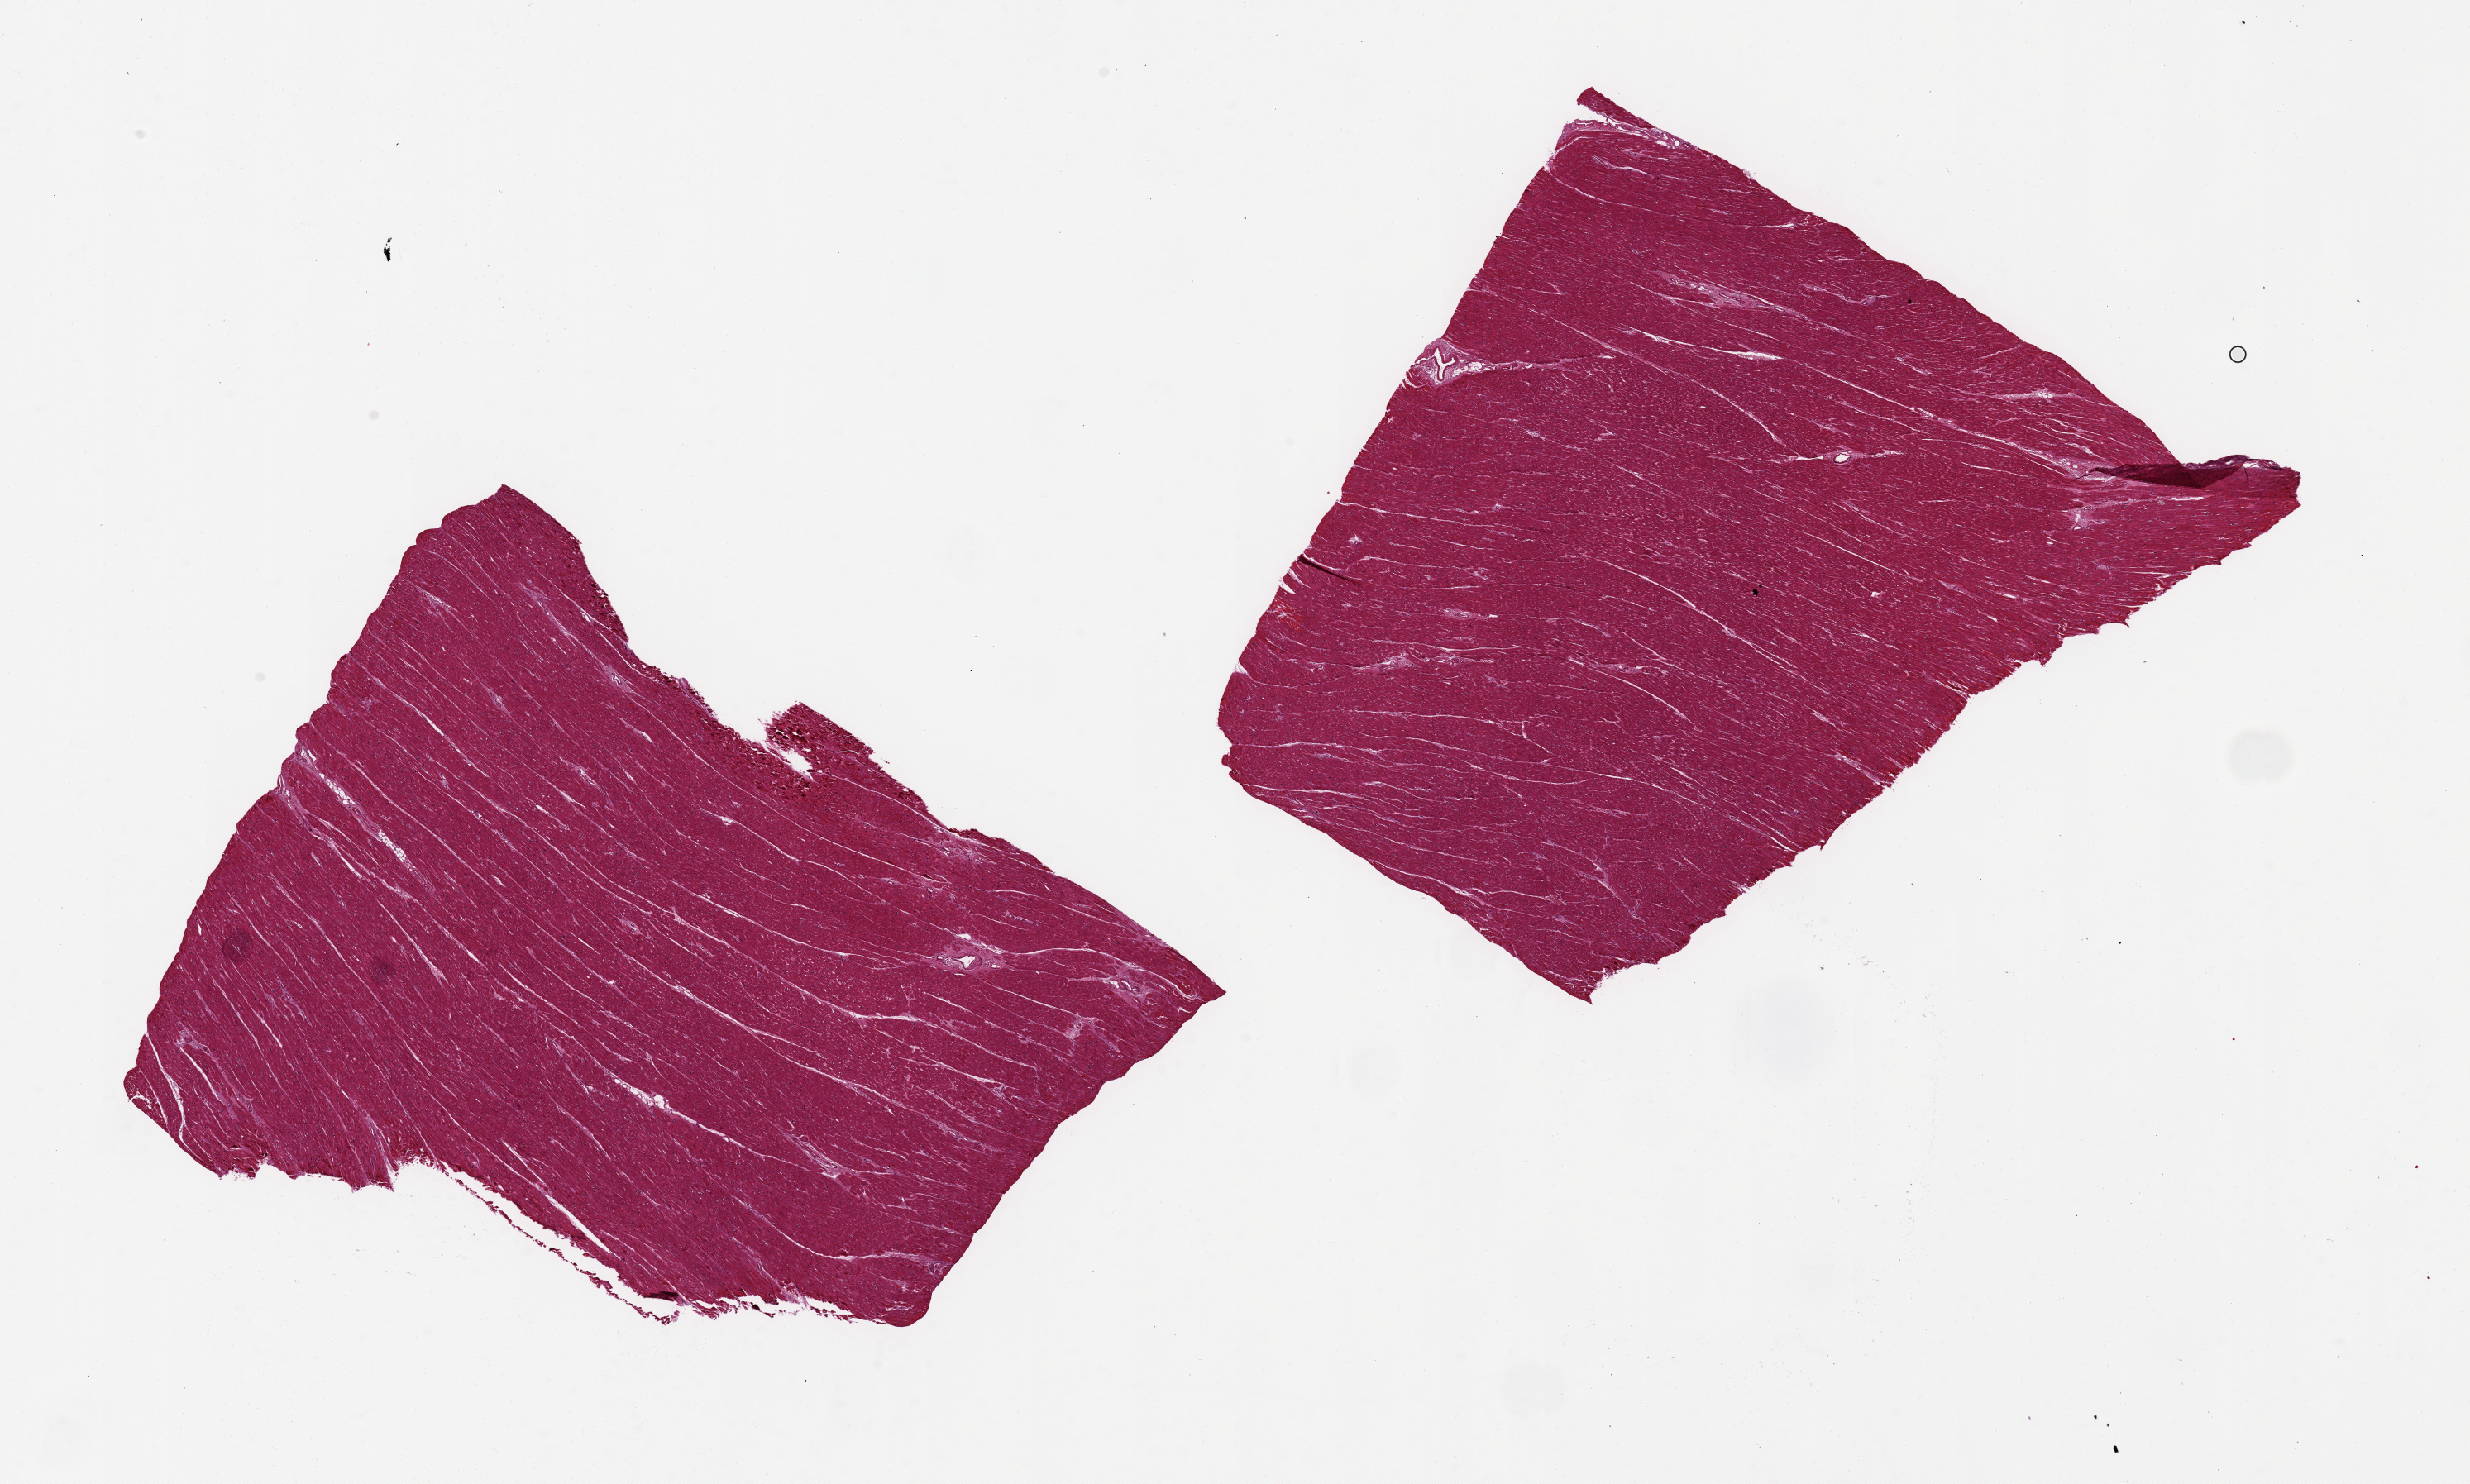
Haematoxylin and eosin whole-slide image, brightfield — low-resolution overview of the scanned area, about 23.6 x 14.2 mm (slide scanned at 20x); PAXgene-fixed paraffin-embedded (PFPE) section; section of heart (target tissue); tissue donor sample. Donor: male.
Pathologist's review note for this sample: 2 pieces 8x6 & 7x7 mm; contraction bands; no fibrosis or fat.